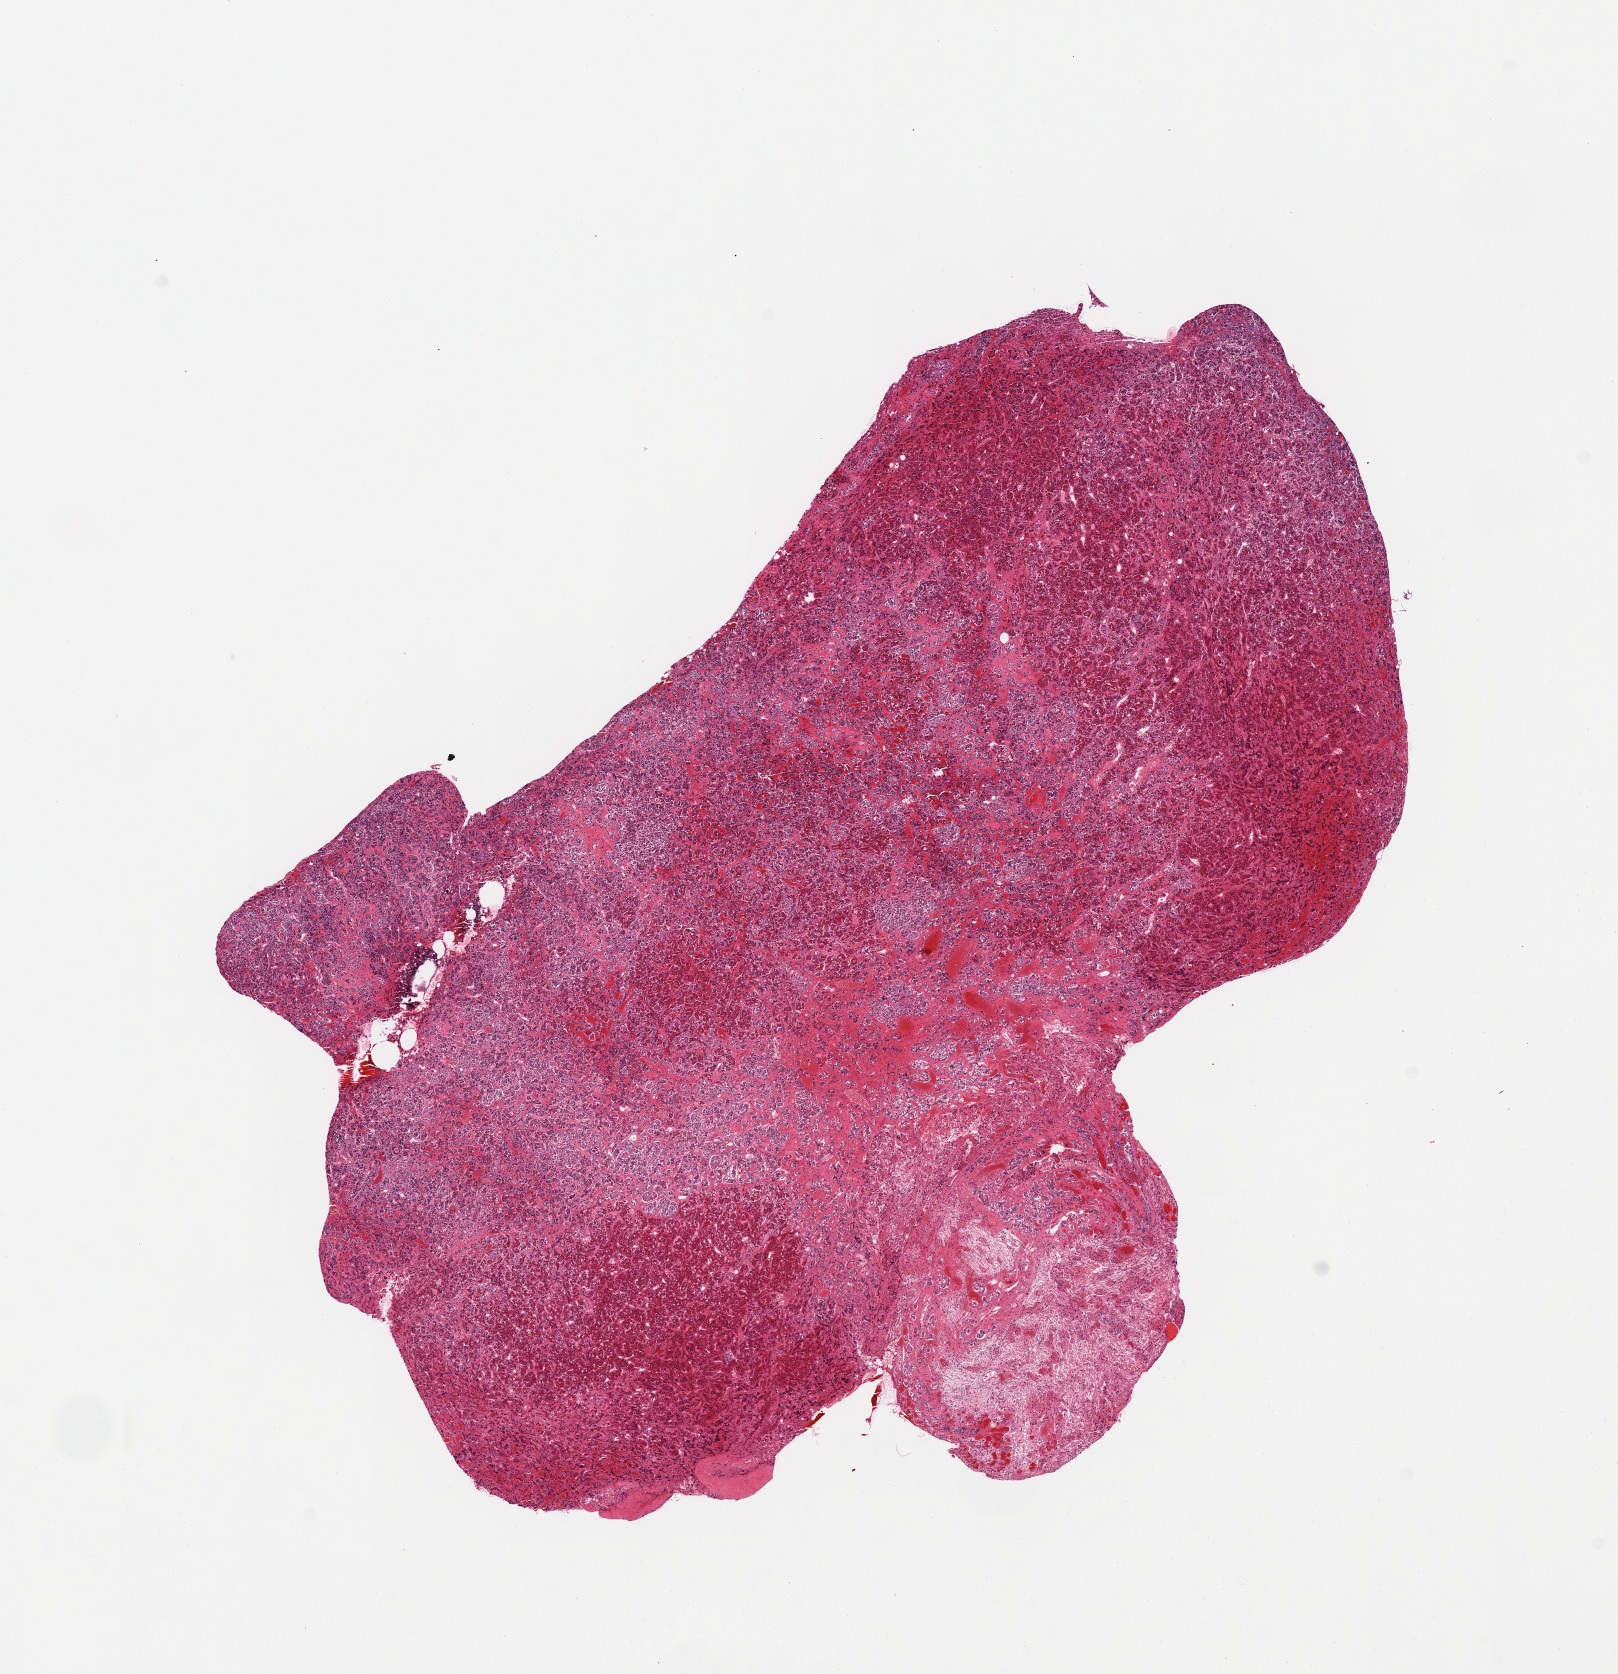
Whole-slide image, hematoxylin and eosin (H&E) stain, a low-resolution overview of the entire scanned area, about 12.8 x 13.2 mm (acquisition: 20x scan). PAXgene-fixed paraffin-embedded (PFPE) section. Target tissue: pituitary. Donor tissue sample. Donor: male.
Reviewer comment on this tissue sample: 1 piece, mainly adenohypophysis, minute nubbin of neurohypophysis.